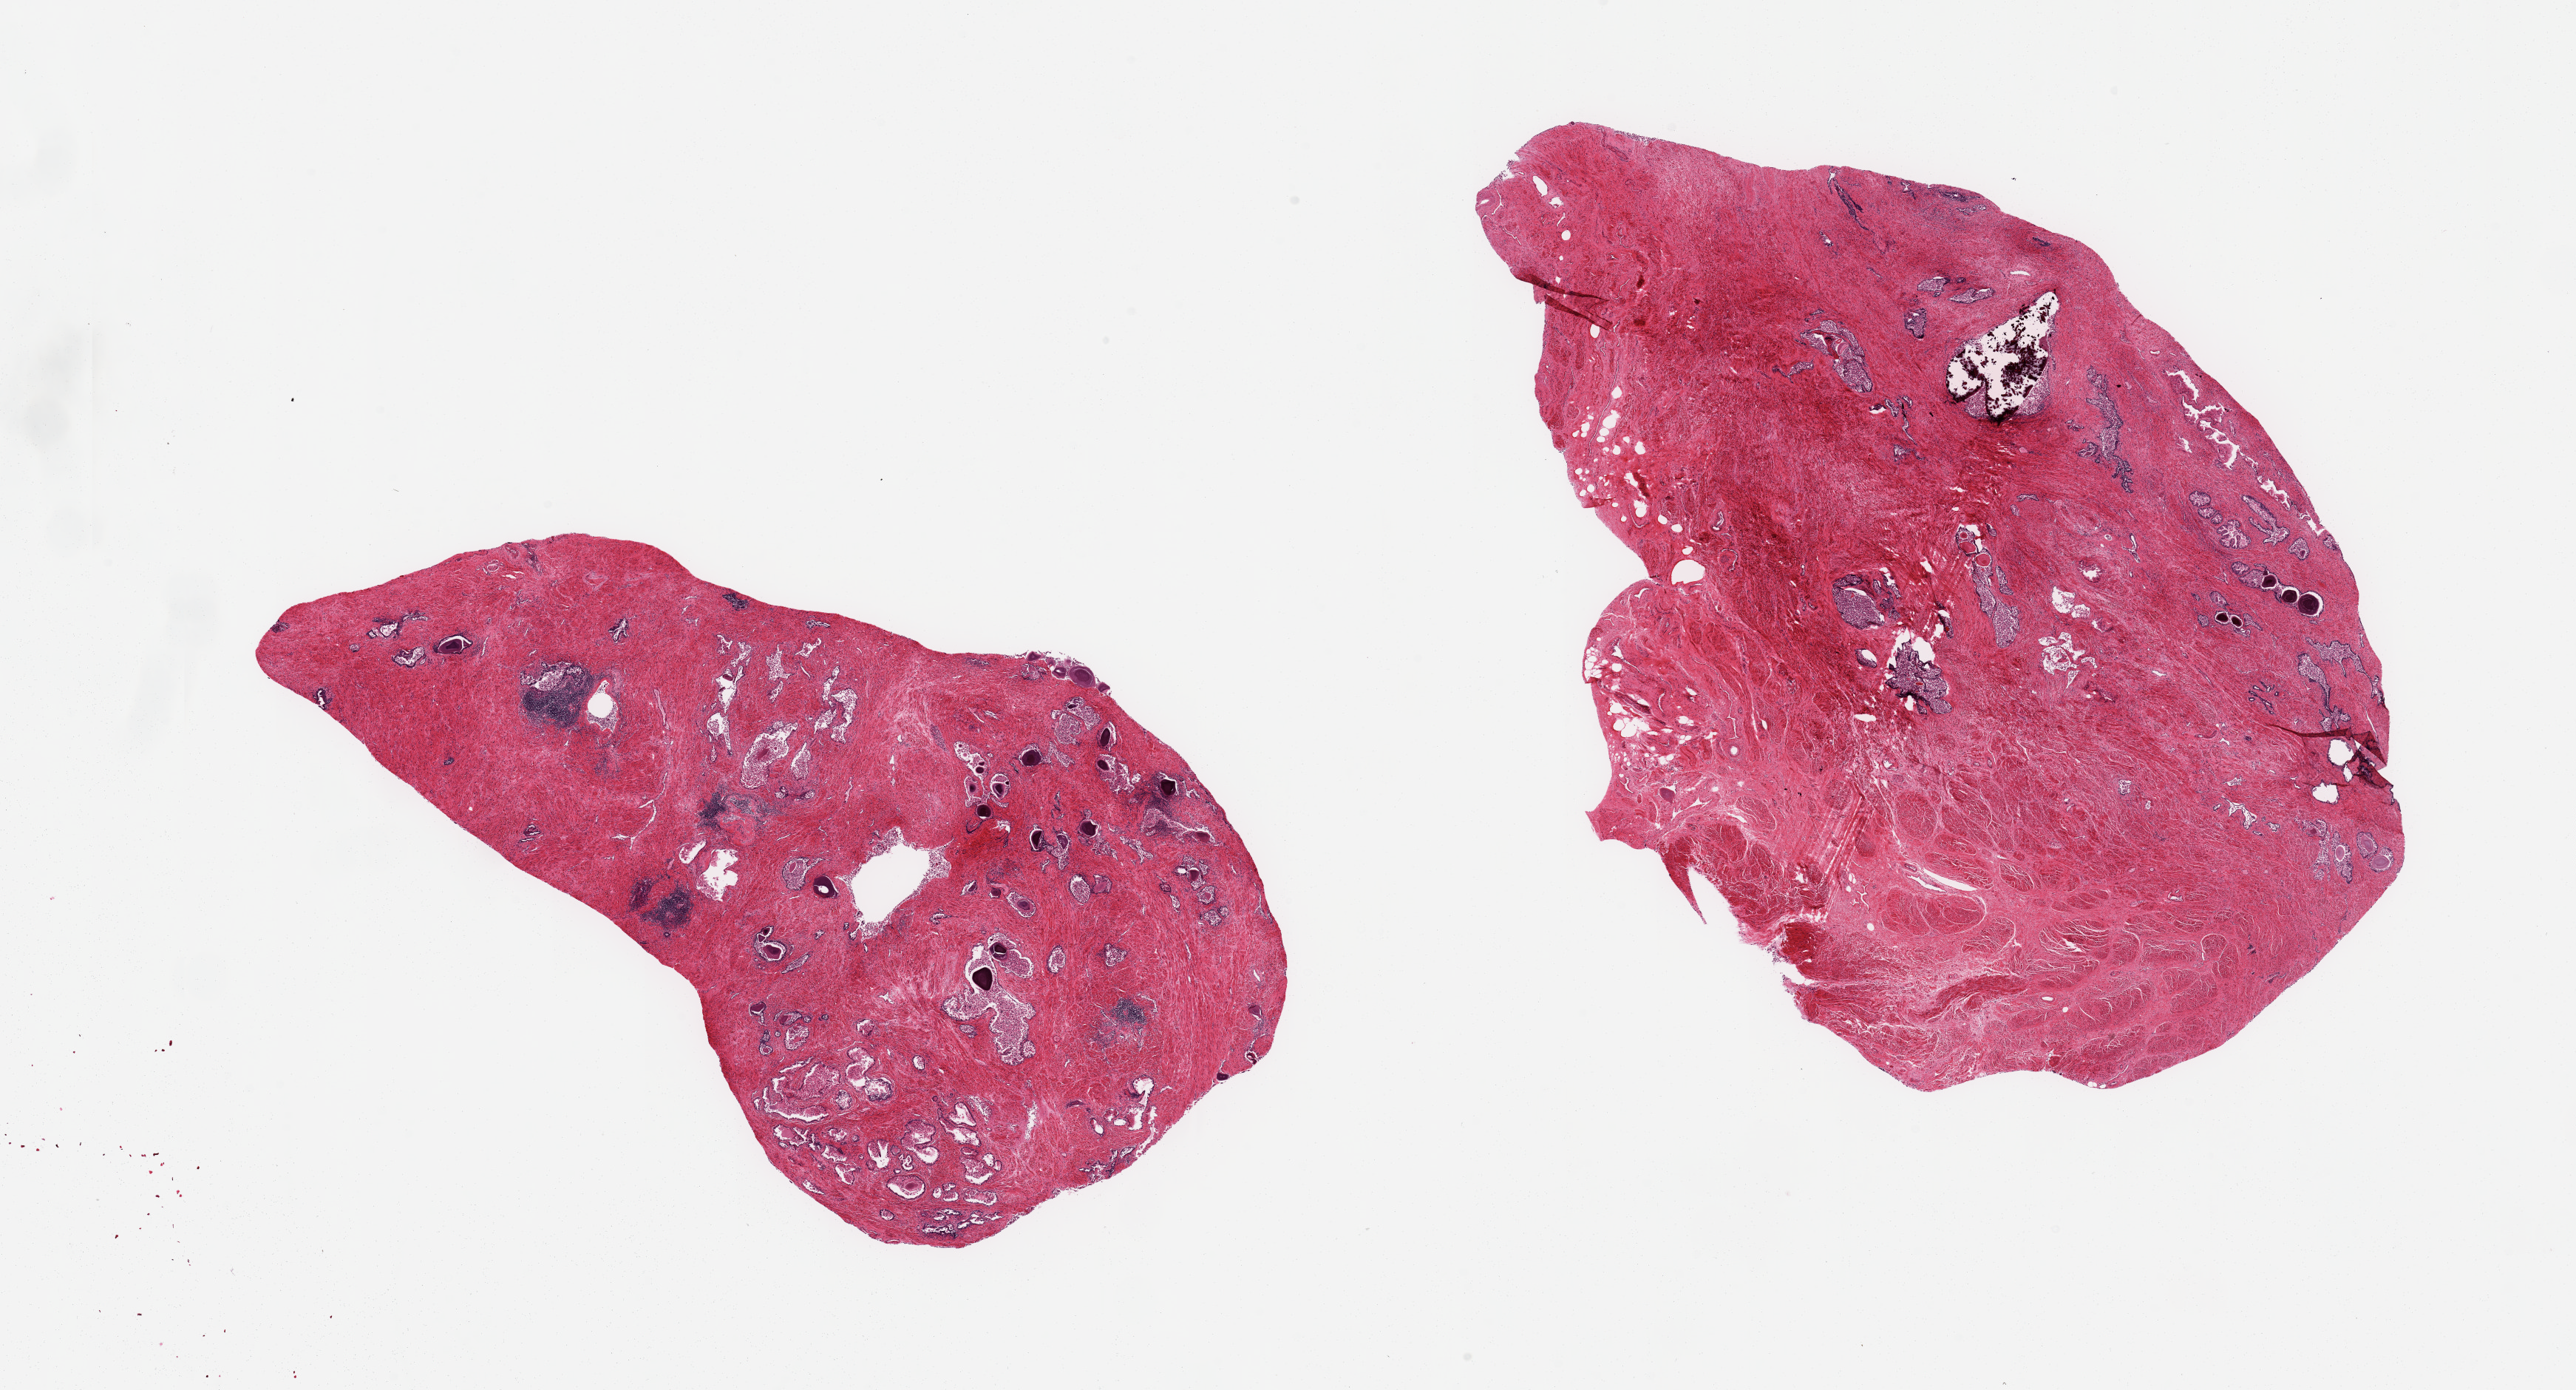
Digitized hematoxylin and eosin (H&E)-stained section, whole scanned area (about 27.6 x 14.9 mm, from a 20x scan) shown as a low-resolution overview. PAXgene-fixed paraffin-embedded (PFPE) section. Target tissue: prostate. Tissue donor sample. Donor sex: male.
* pathologist's review note for this sample: 2 pieces; acini autolyzed; stroma intact; foci of chronic inflammation